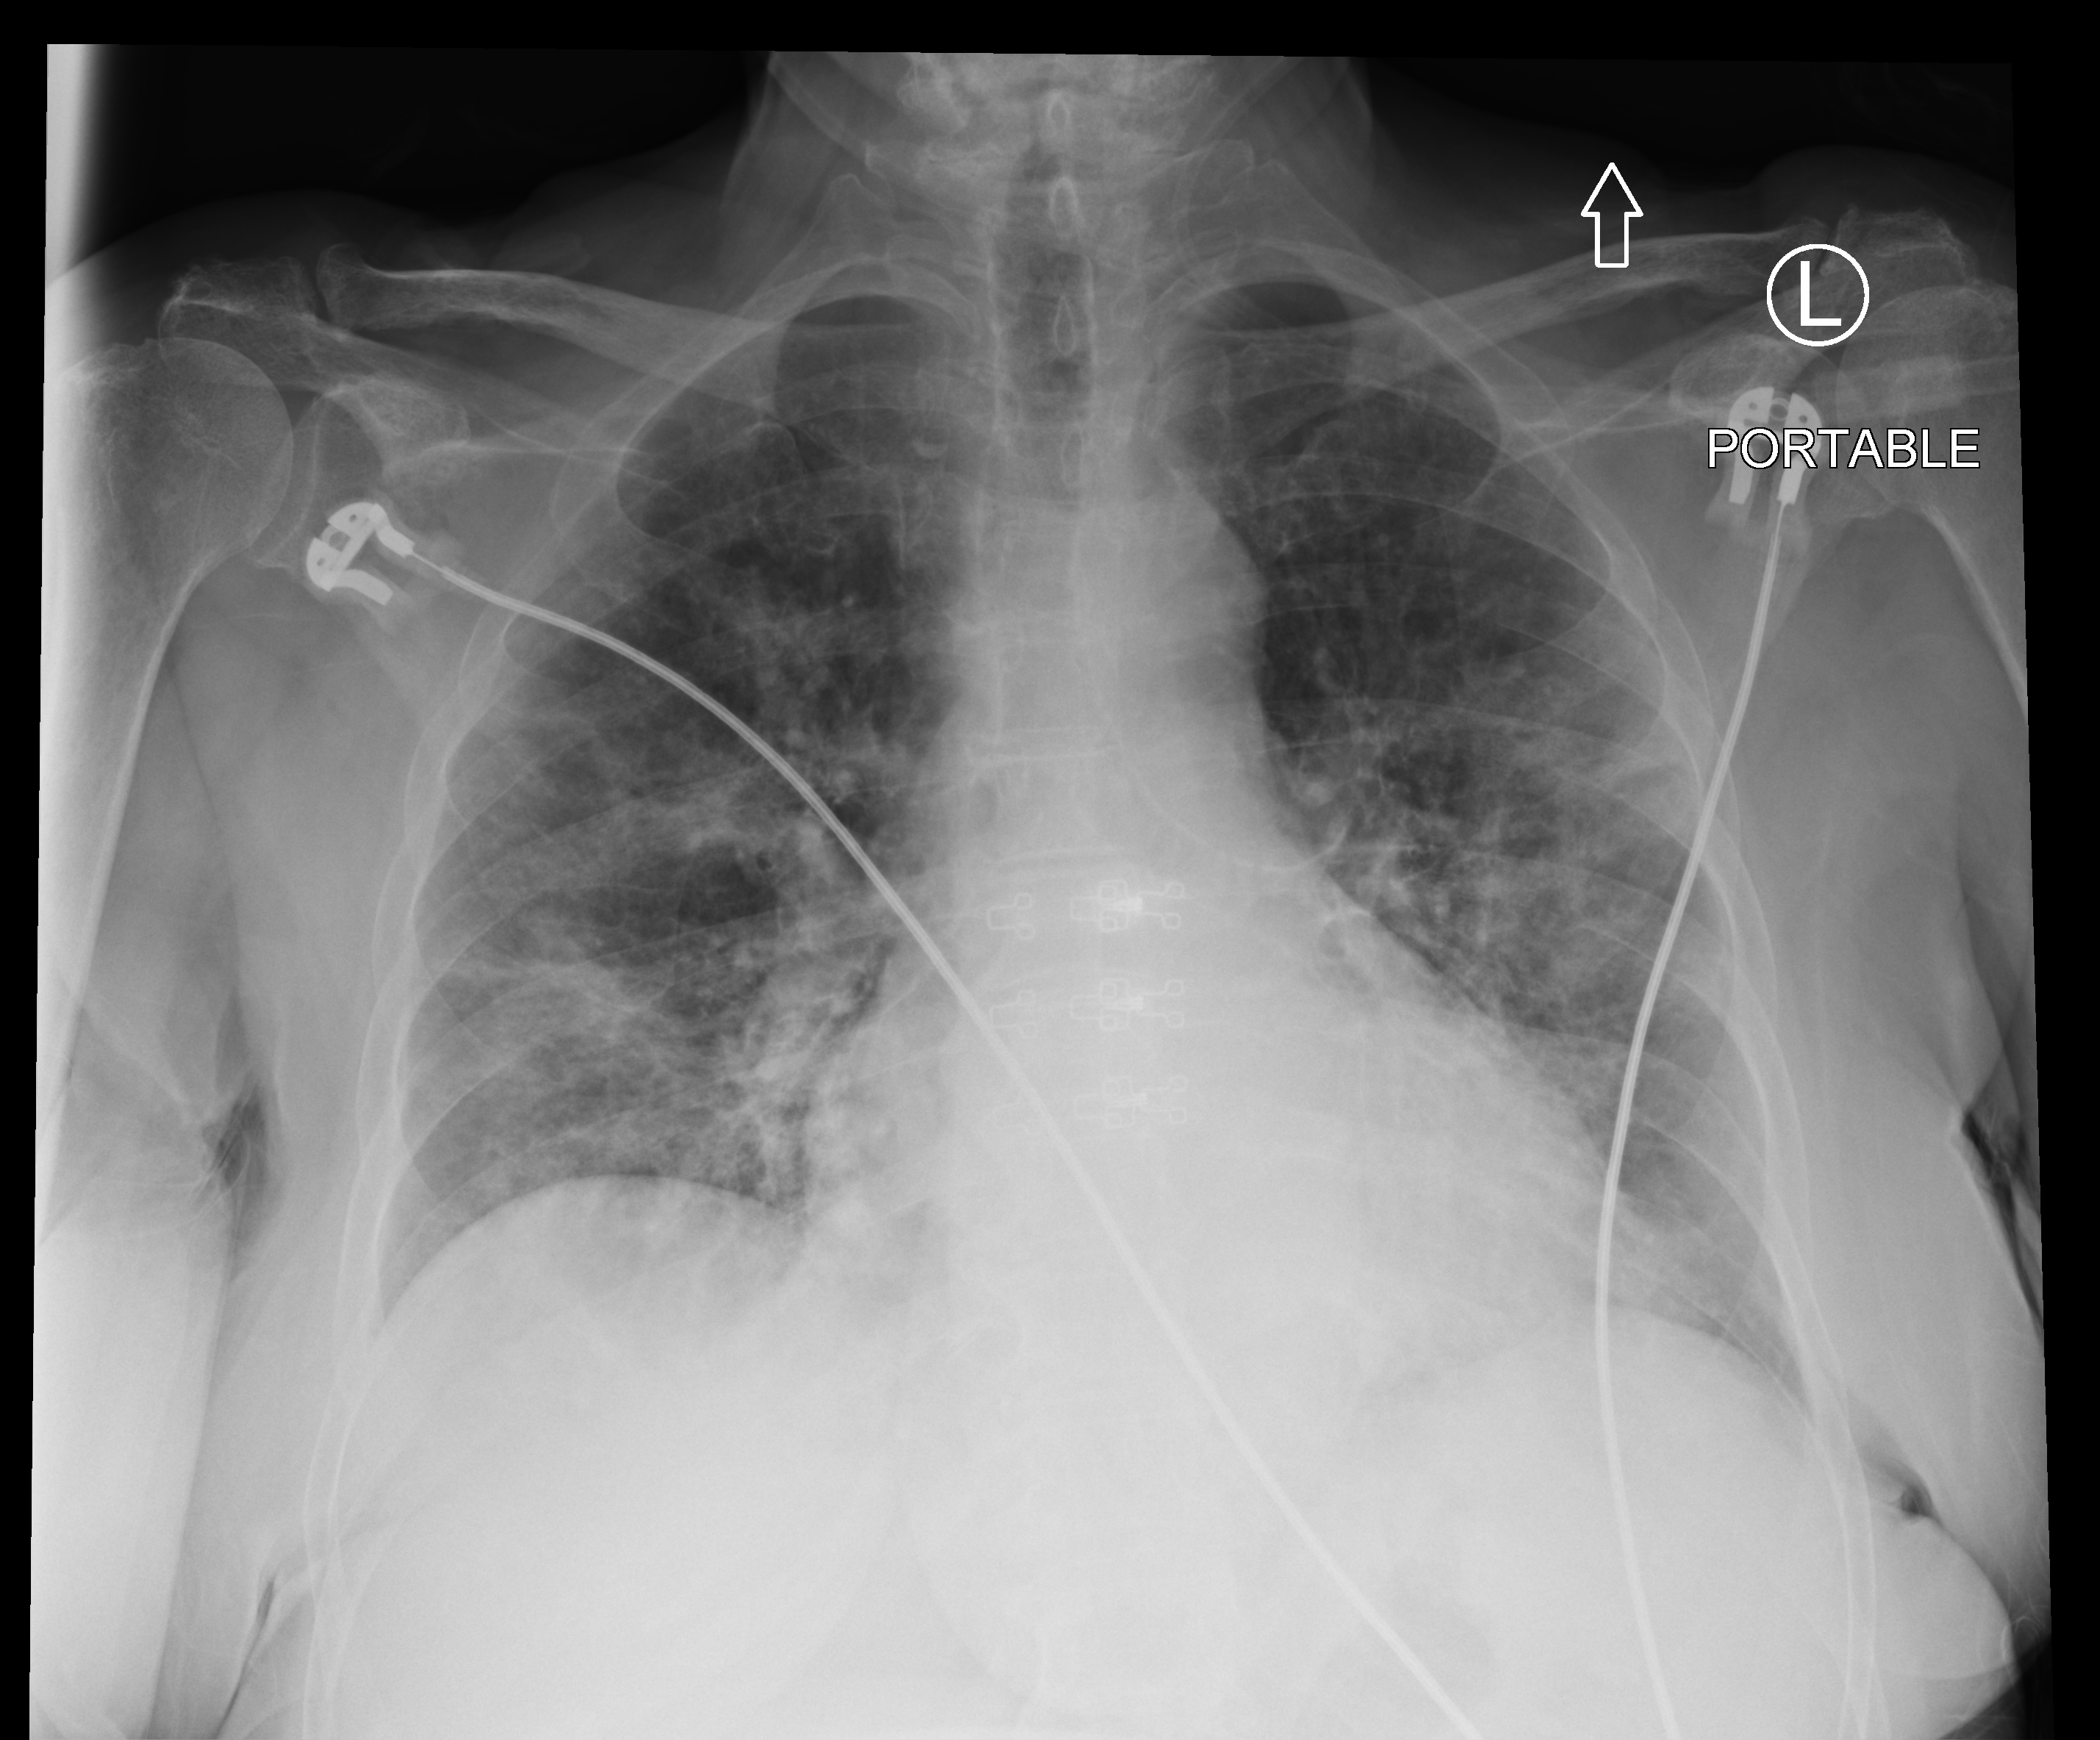
Bedside chest radiograph (computed radiography), anteroposterior (AP) projection. Female patient hospitalised with COVID-19, age 60–74 years.
Hospital-stay facts (about this admission, not read from this image; timing relative to this image not recorded): other chronic lung disease (admission record): no.